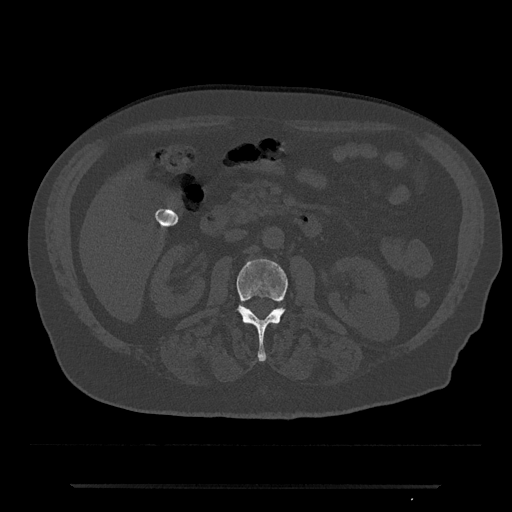
CT including the spine, one axial slice; position 468 of 797 along the scan axis; reconstruction kernel Br40s/3; 120 kVp; bone window (W 1800 / L 400 HU); 0.5 mm slice thickness; 512 × 512 image matrix, field of view 434 × 434 mm. Patient: male, 80 years. Case-level facts recorded for this patient, not image findings: primary cancer: prostate.
Annotated regions visible in this slice (semi-automatic segmentation, software-assisted and operator-edited):
- L2 vertebra: box from (x=236, y=259) to (x=288, y=362) px